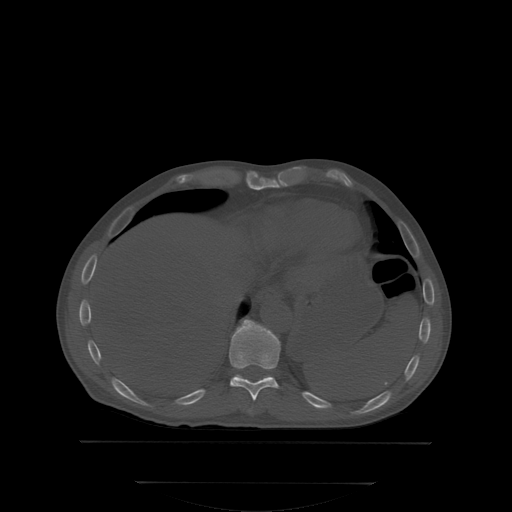
CT including the spine, one axial slice; slice 192 of 350 in the series (ordered by position); bone window (W 1800 / L 400 HU); 2.5 mm slice thickness; 512 × 512 image matrix, field of view 500 × 500 mm. Male patient, age 58 years. Case-level facts recorded for this patient, not image findings: primary cancer: prostate; vertebrae with lytic lesions (as recorded): L1.
Annotated regions visible in this slice (semi-automatic segmentation, software-assisted and operator-edited):
- T10 vertebra: box from (x=230, y=321) to (x=279, y=400) px
- T9 vertebra: (x=249, y=407)–(x=253, y=412)